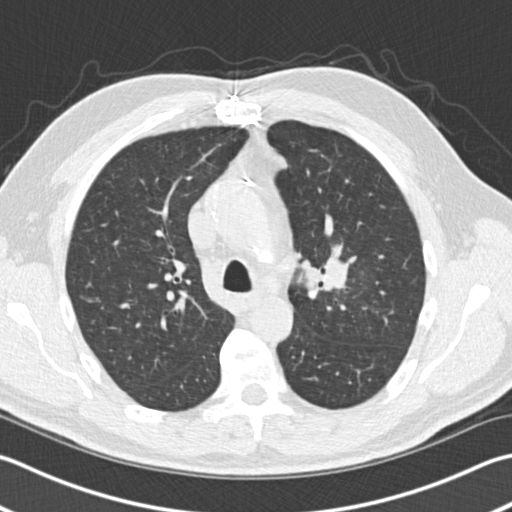
Low-dose screening chest CT, one axial slice; position 104 of 153 along the scan axis; reconstruction kernel B30f; 120 kVp; lung window (W 1500 / L -600 HU); 2 mm slice thickness; 512 × 512 image matrix, field of view 346 × 346 mm.
Structures marked on this image (expert manual segmentation):
- lesion 1 (tumor, upper lobe of left lung): bounding box (x1, y1, x2, y2) in pixels: (326, 259, 350, 286)